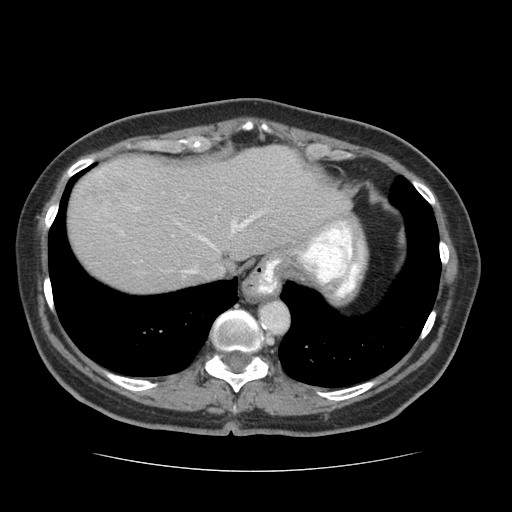
Contrast-enhanced abdominal CT (liver protocol), one axial slice; slice 59 of 75 in the series (ordered by position); reconstruction kernel STANDARD; soft-tissue window (W 400 / L 40 HU); 512 × 512 image matrix. From the clinical record (not read from this slice): diagnosis: hepatocellular carcinoma (patient treated with transarterial chemoembolisation; whether this scan precedes or follows treatment is not stated here); TNM stage (as recorded): Stage-I; Child-Pugh class: A; tumour differentiation: moderately differentiated; tumour nodularity: uninodular.
Structures marked on this image (semi-automatically segmented with operator editing):
- abdominal aorta: bounding box <260,301,289,333> (left, top, right, bottom; pixels)
- liver parenchyma outside the tumour (the mass and vessels are separate outlines, so this box may not span the whole liver): <68,146,350,292>
- liver vessels: <97,171,261,274>